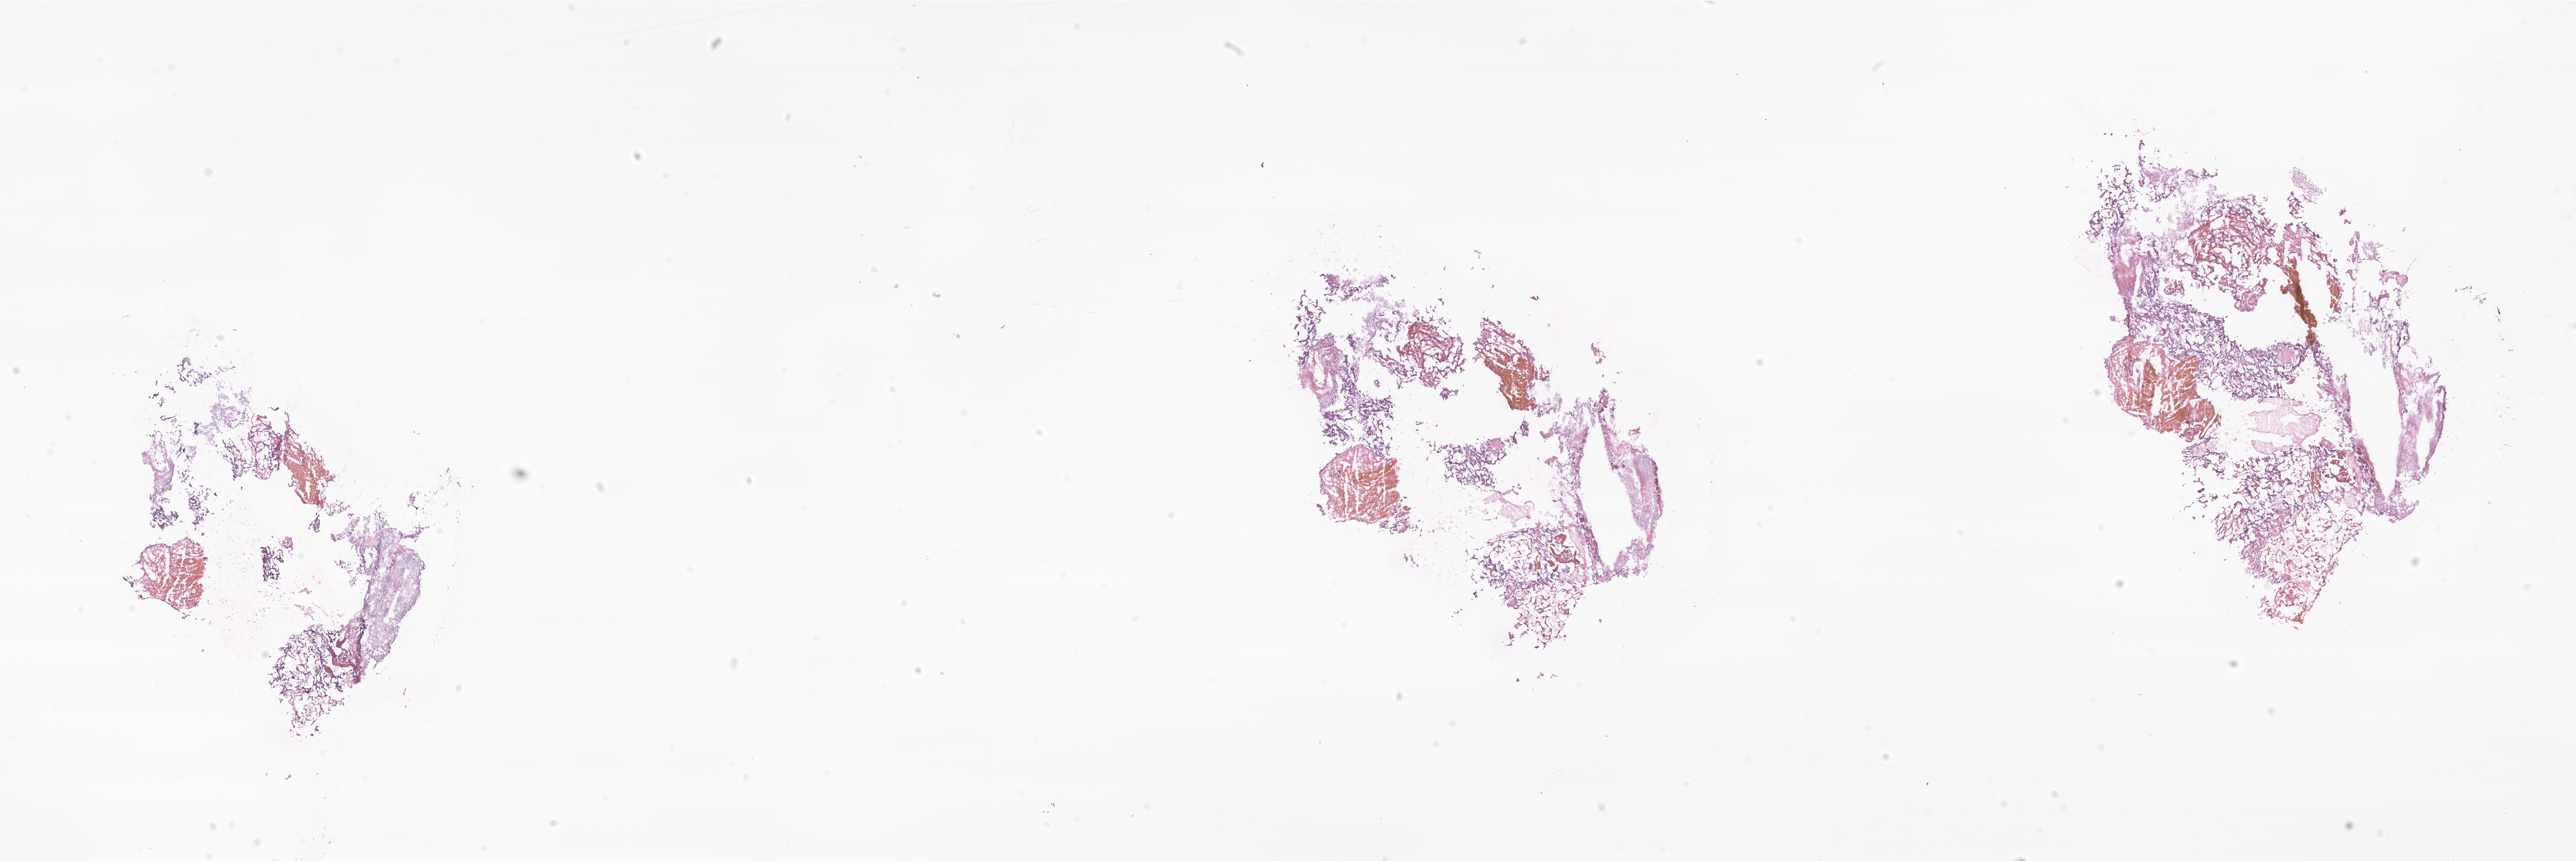
Whole-slide image, hematoxylin and eosin (H&E) stain of tumor tissue from the temporal lobe — whole scanned area (about 38.3 x 12.8 mm) shown as a low-resolution overview, cryosection (OCT / tissue freezing medium). Patient: female, age 51 months (4 years 3 months).
• diagnosis: Neuroblastoma, NOS